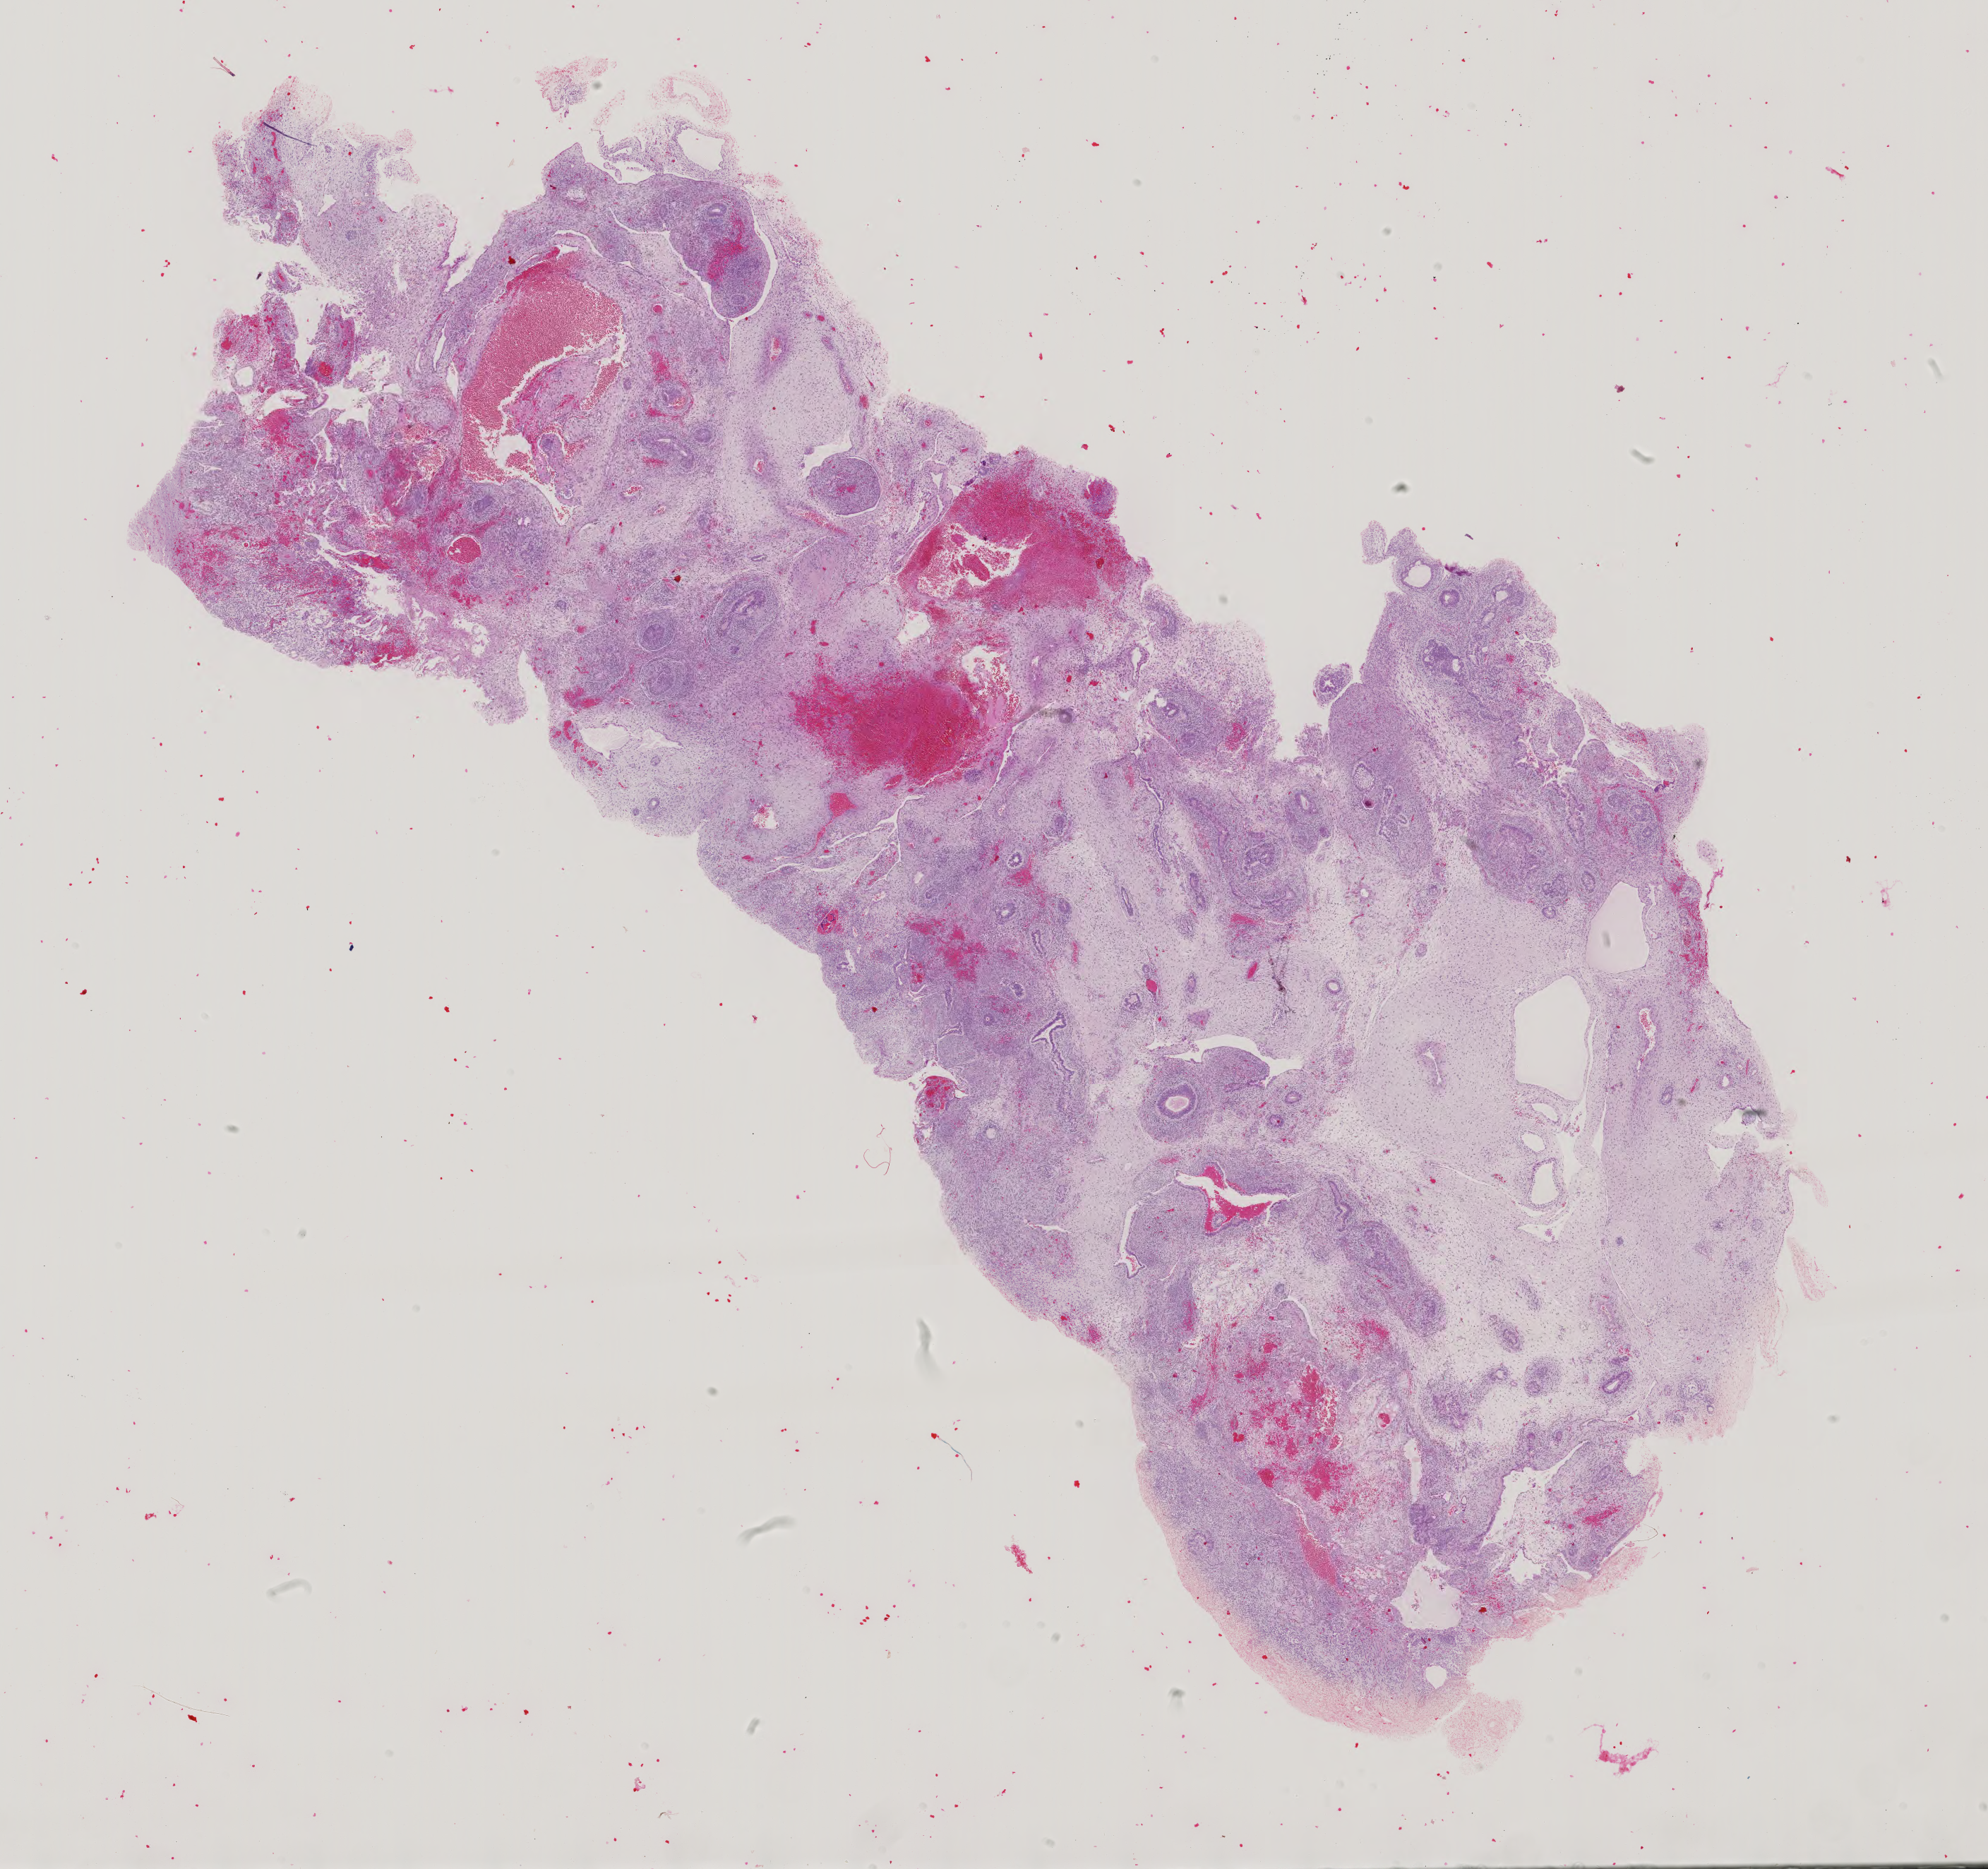
H&E-stained whole-slide image, whole scanned area (about 20.5 x 19.3 mm, slide scanned at 40x) shown as a low-resolution overview. Male patient.
- specimen: formalin-fixed paraffin-embedded (FFPE) diagnostic section; testis, primary tumour sample